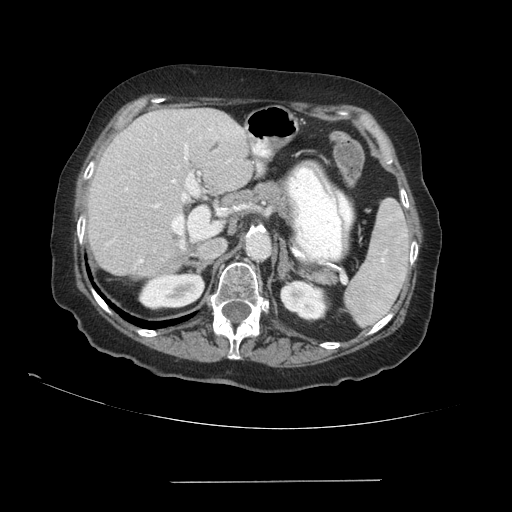
Contrast-enhanced abdominal CT (liver protocol), one axial slice. Position 58 of 89 along the scan axis. Reconstruction kernel STANDARD. Soft-tissue window (W 400 / L 40 HU). 2.5 mm slice thickness. 512 × 512 image matrix, field of view 400 × 400 mm. From the clinical record (not read from this slice): diagnosis: hepatocellular carcinoma (patient treated with transarterial chemoembolisation; whether this scan precedes or follows treatment is not stated here); TNM stage (as recorded): Stage-IVA; Child-Pugh class: A.
Structures marked on this image (semi-automatic segmentation, software-assisted and operator-edited):
- liver parenchyma outside the tumour (the mass and vessels are separate outlines, so this box may not span the whole liver): bounding box (x1, y1, x2, y2) in pixels: (88, 108, 252, 276)
- liver vessels: (139, 129, 243, 263)